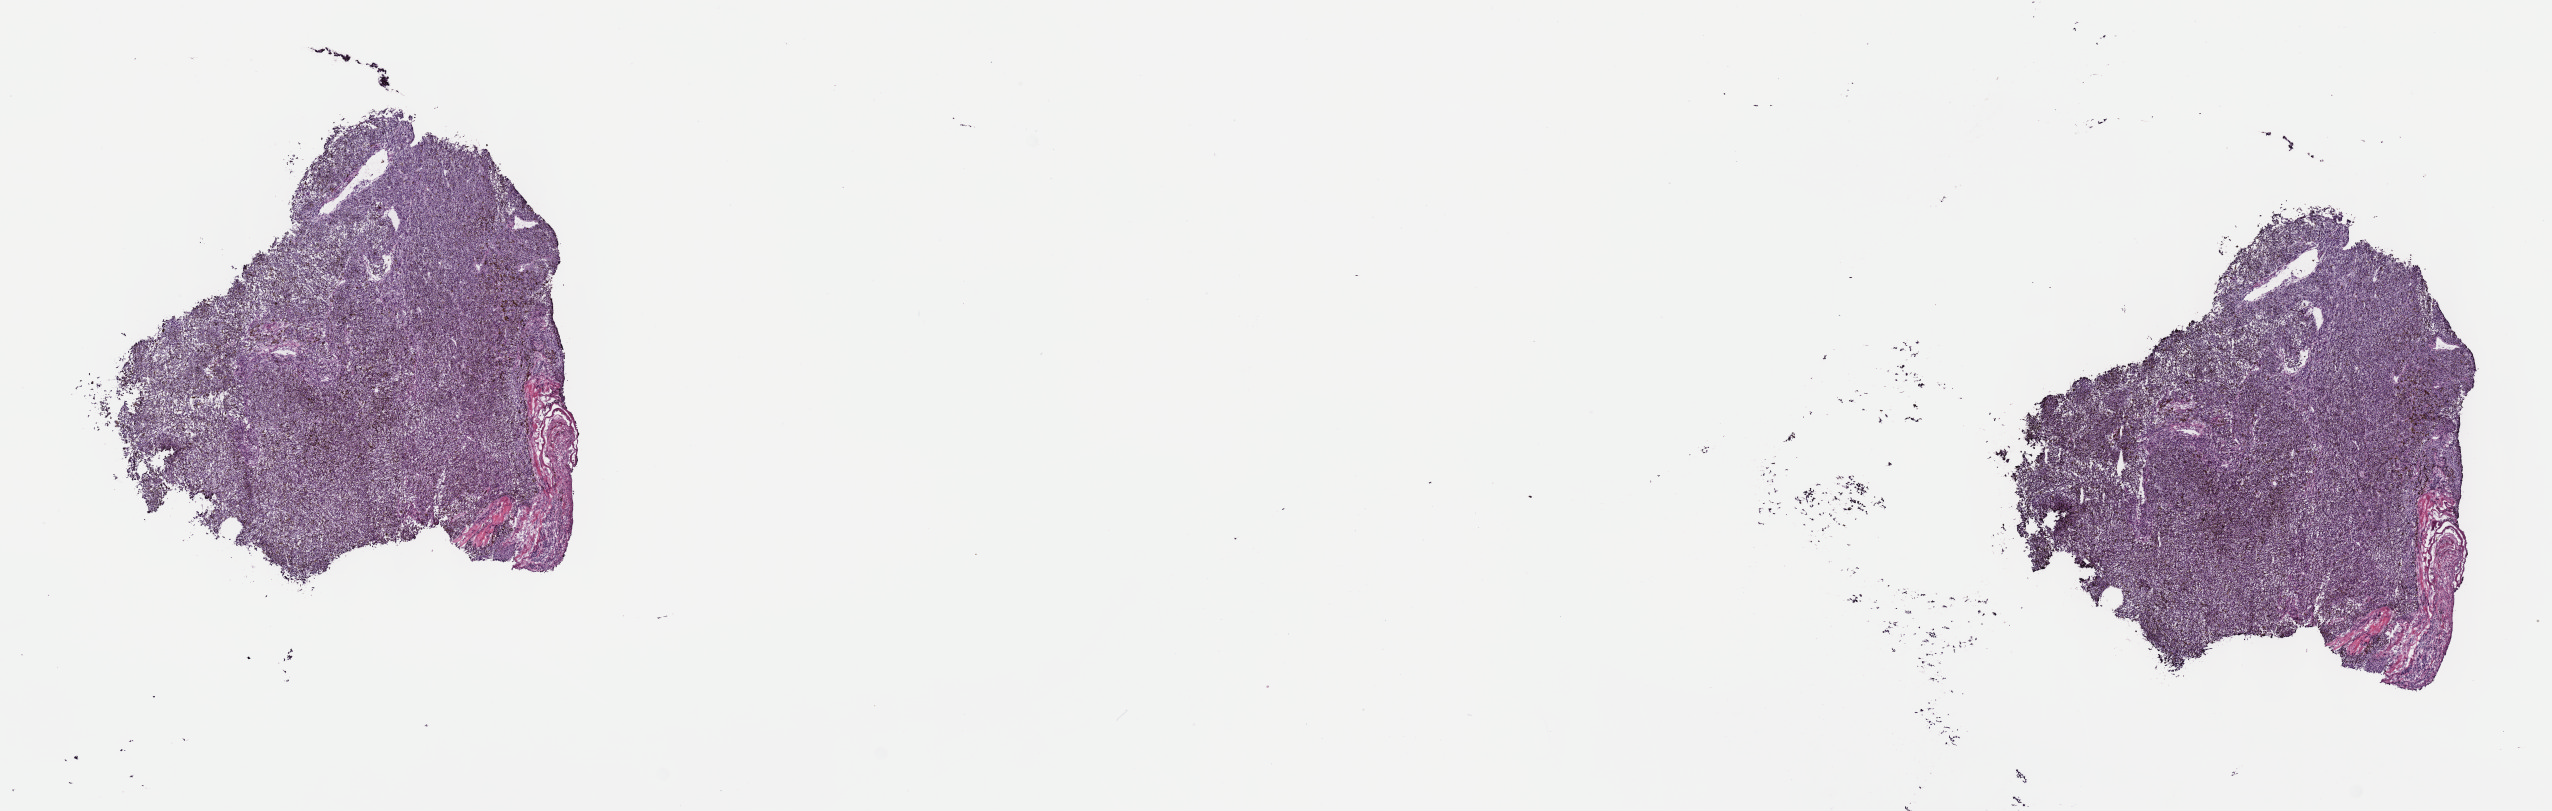
H&E-stained whole-slide image — whole scanned area (about 20.6 x 6.6 mm, slide scanned at 40x) shown as a low-resolution overview; frozen section from the top of the tissue portion; uvea, primary tumour sample. Male, age 86 years at initial diagnosis. Slide review estimates, as recorded: tumour cells 100%, tumour nuclei 80%, normal cells 0%, stromal cells 0%, necrosis 0%. Inflammatory infiltration, as recorded: lymphocyte infiltration 1%, monocyte infiltration 0%, neutrophil infiltration 0%.
AJCC pathologic stage: IIB (7th edition). Pathologic diagnosis: Mixed epithelioid and spindle cell melanoma (choroid).